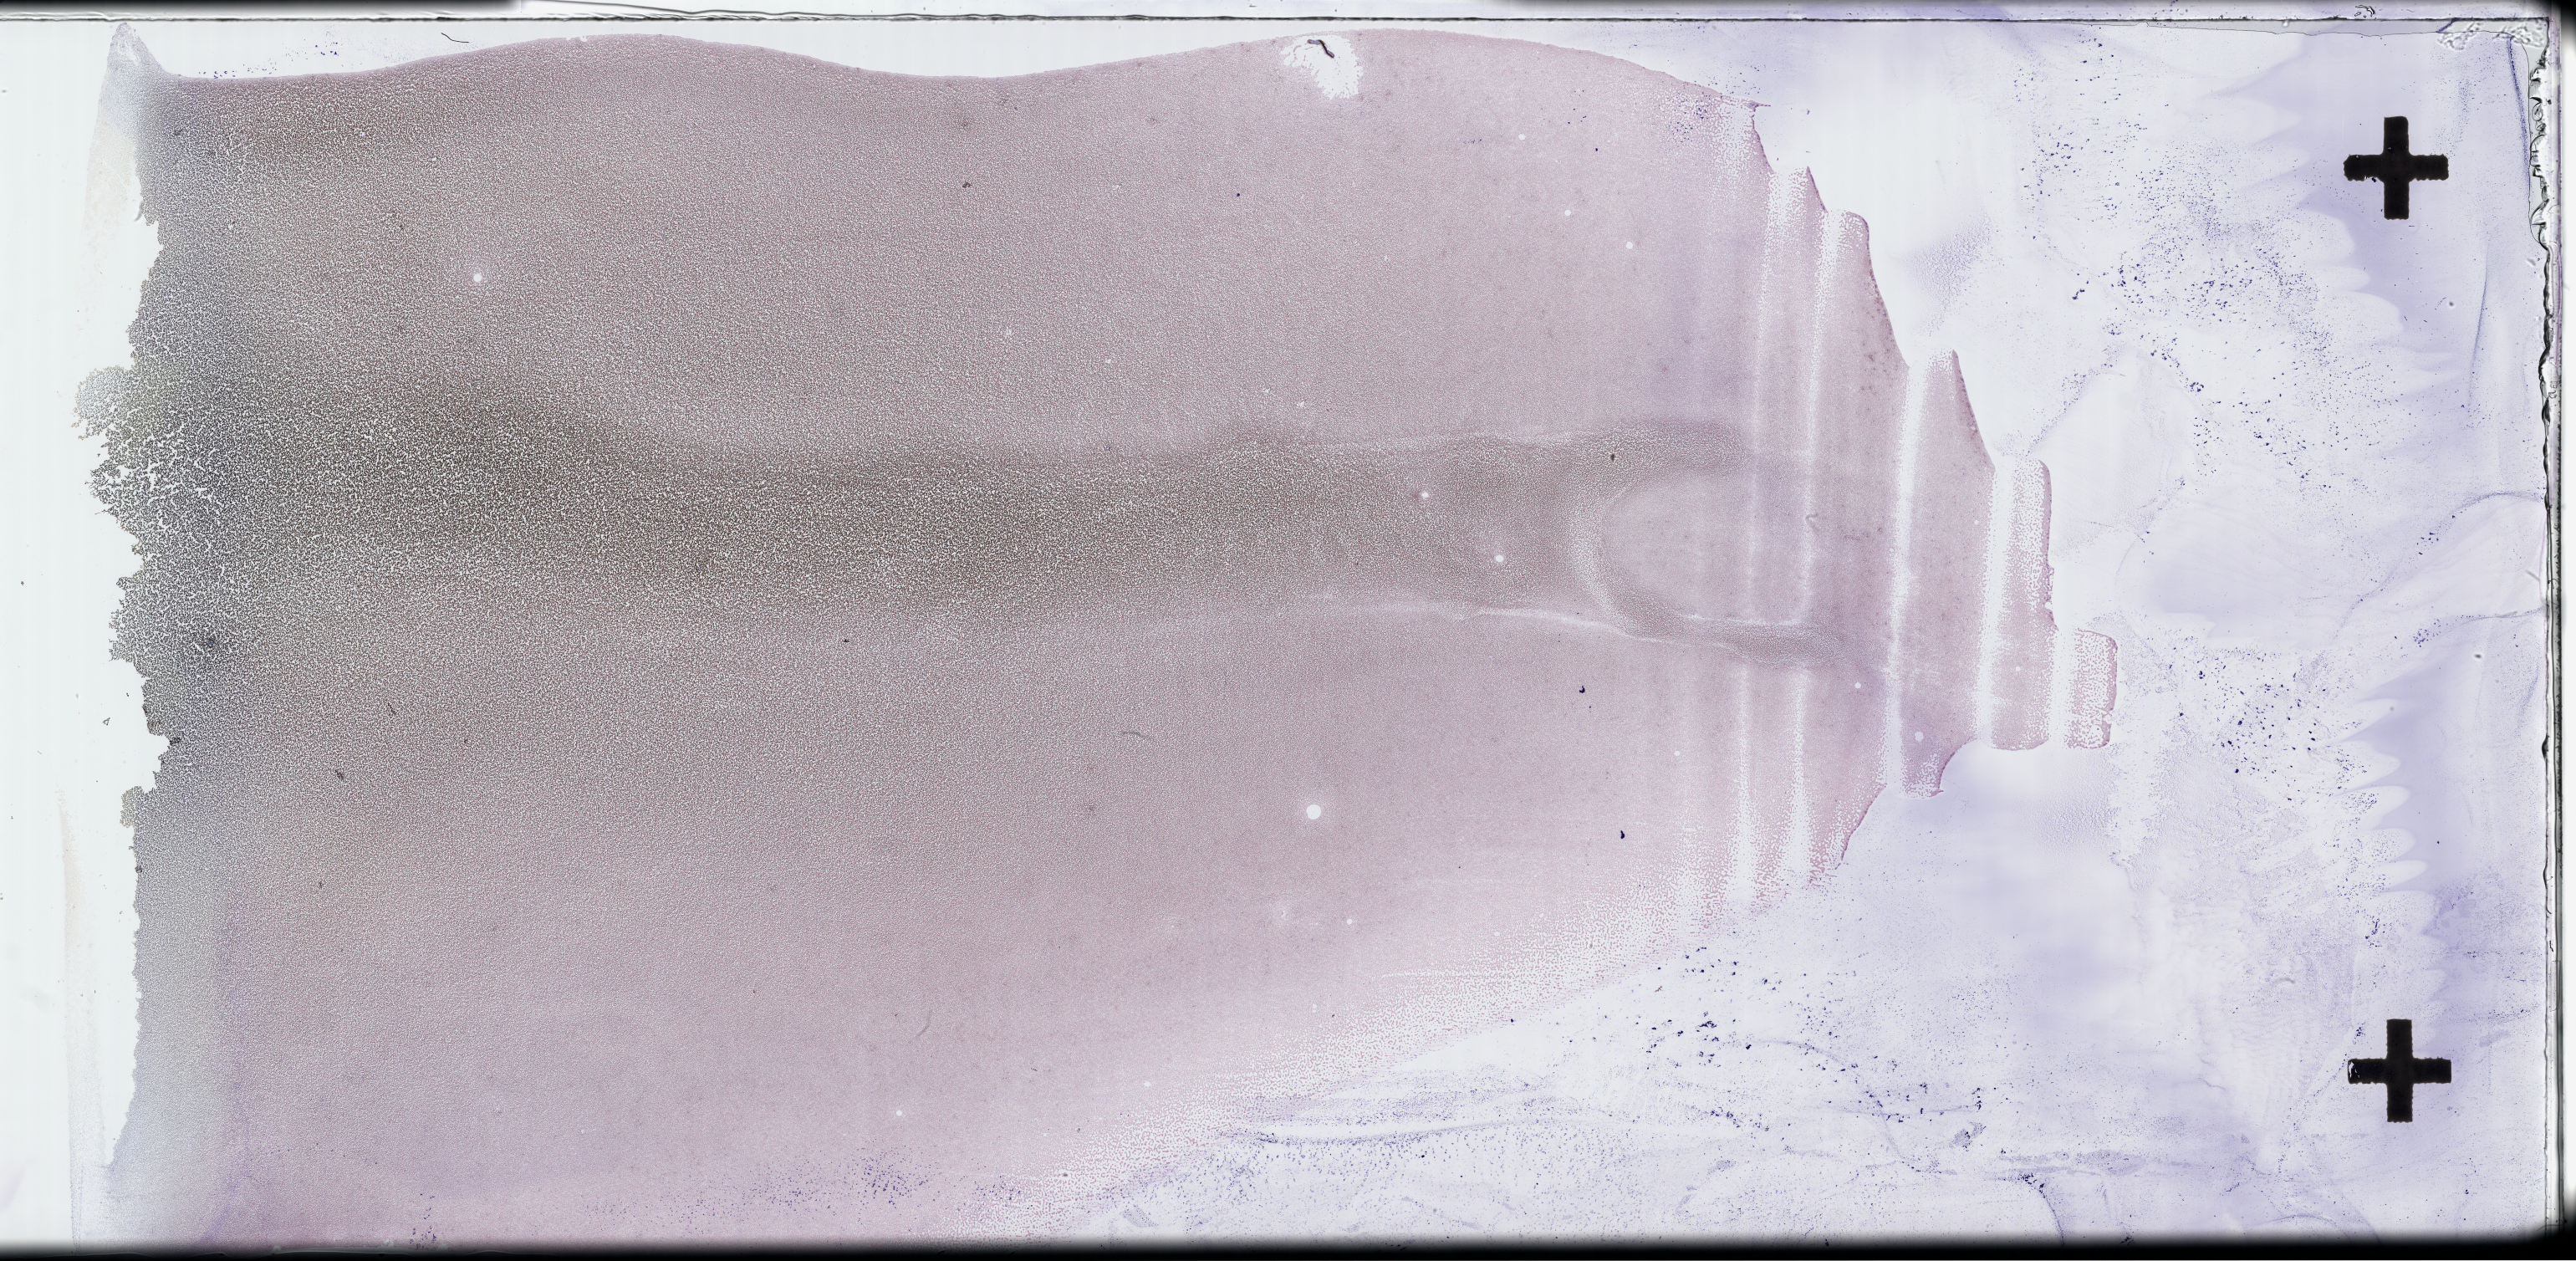
Wright-Giemsa-stained whole blood smear, whole-slide image — shown as a low-resolution overview of the whole scanned area (about 49.8 x 24.4 mm); EDTA-anticoagulated smear; specimen time point: collected at baseline (before treatment). Female patient.
From a patient with: Plasma Cell Myeloma.